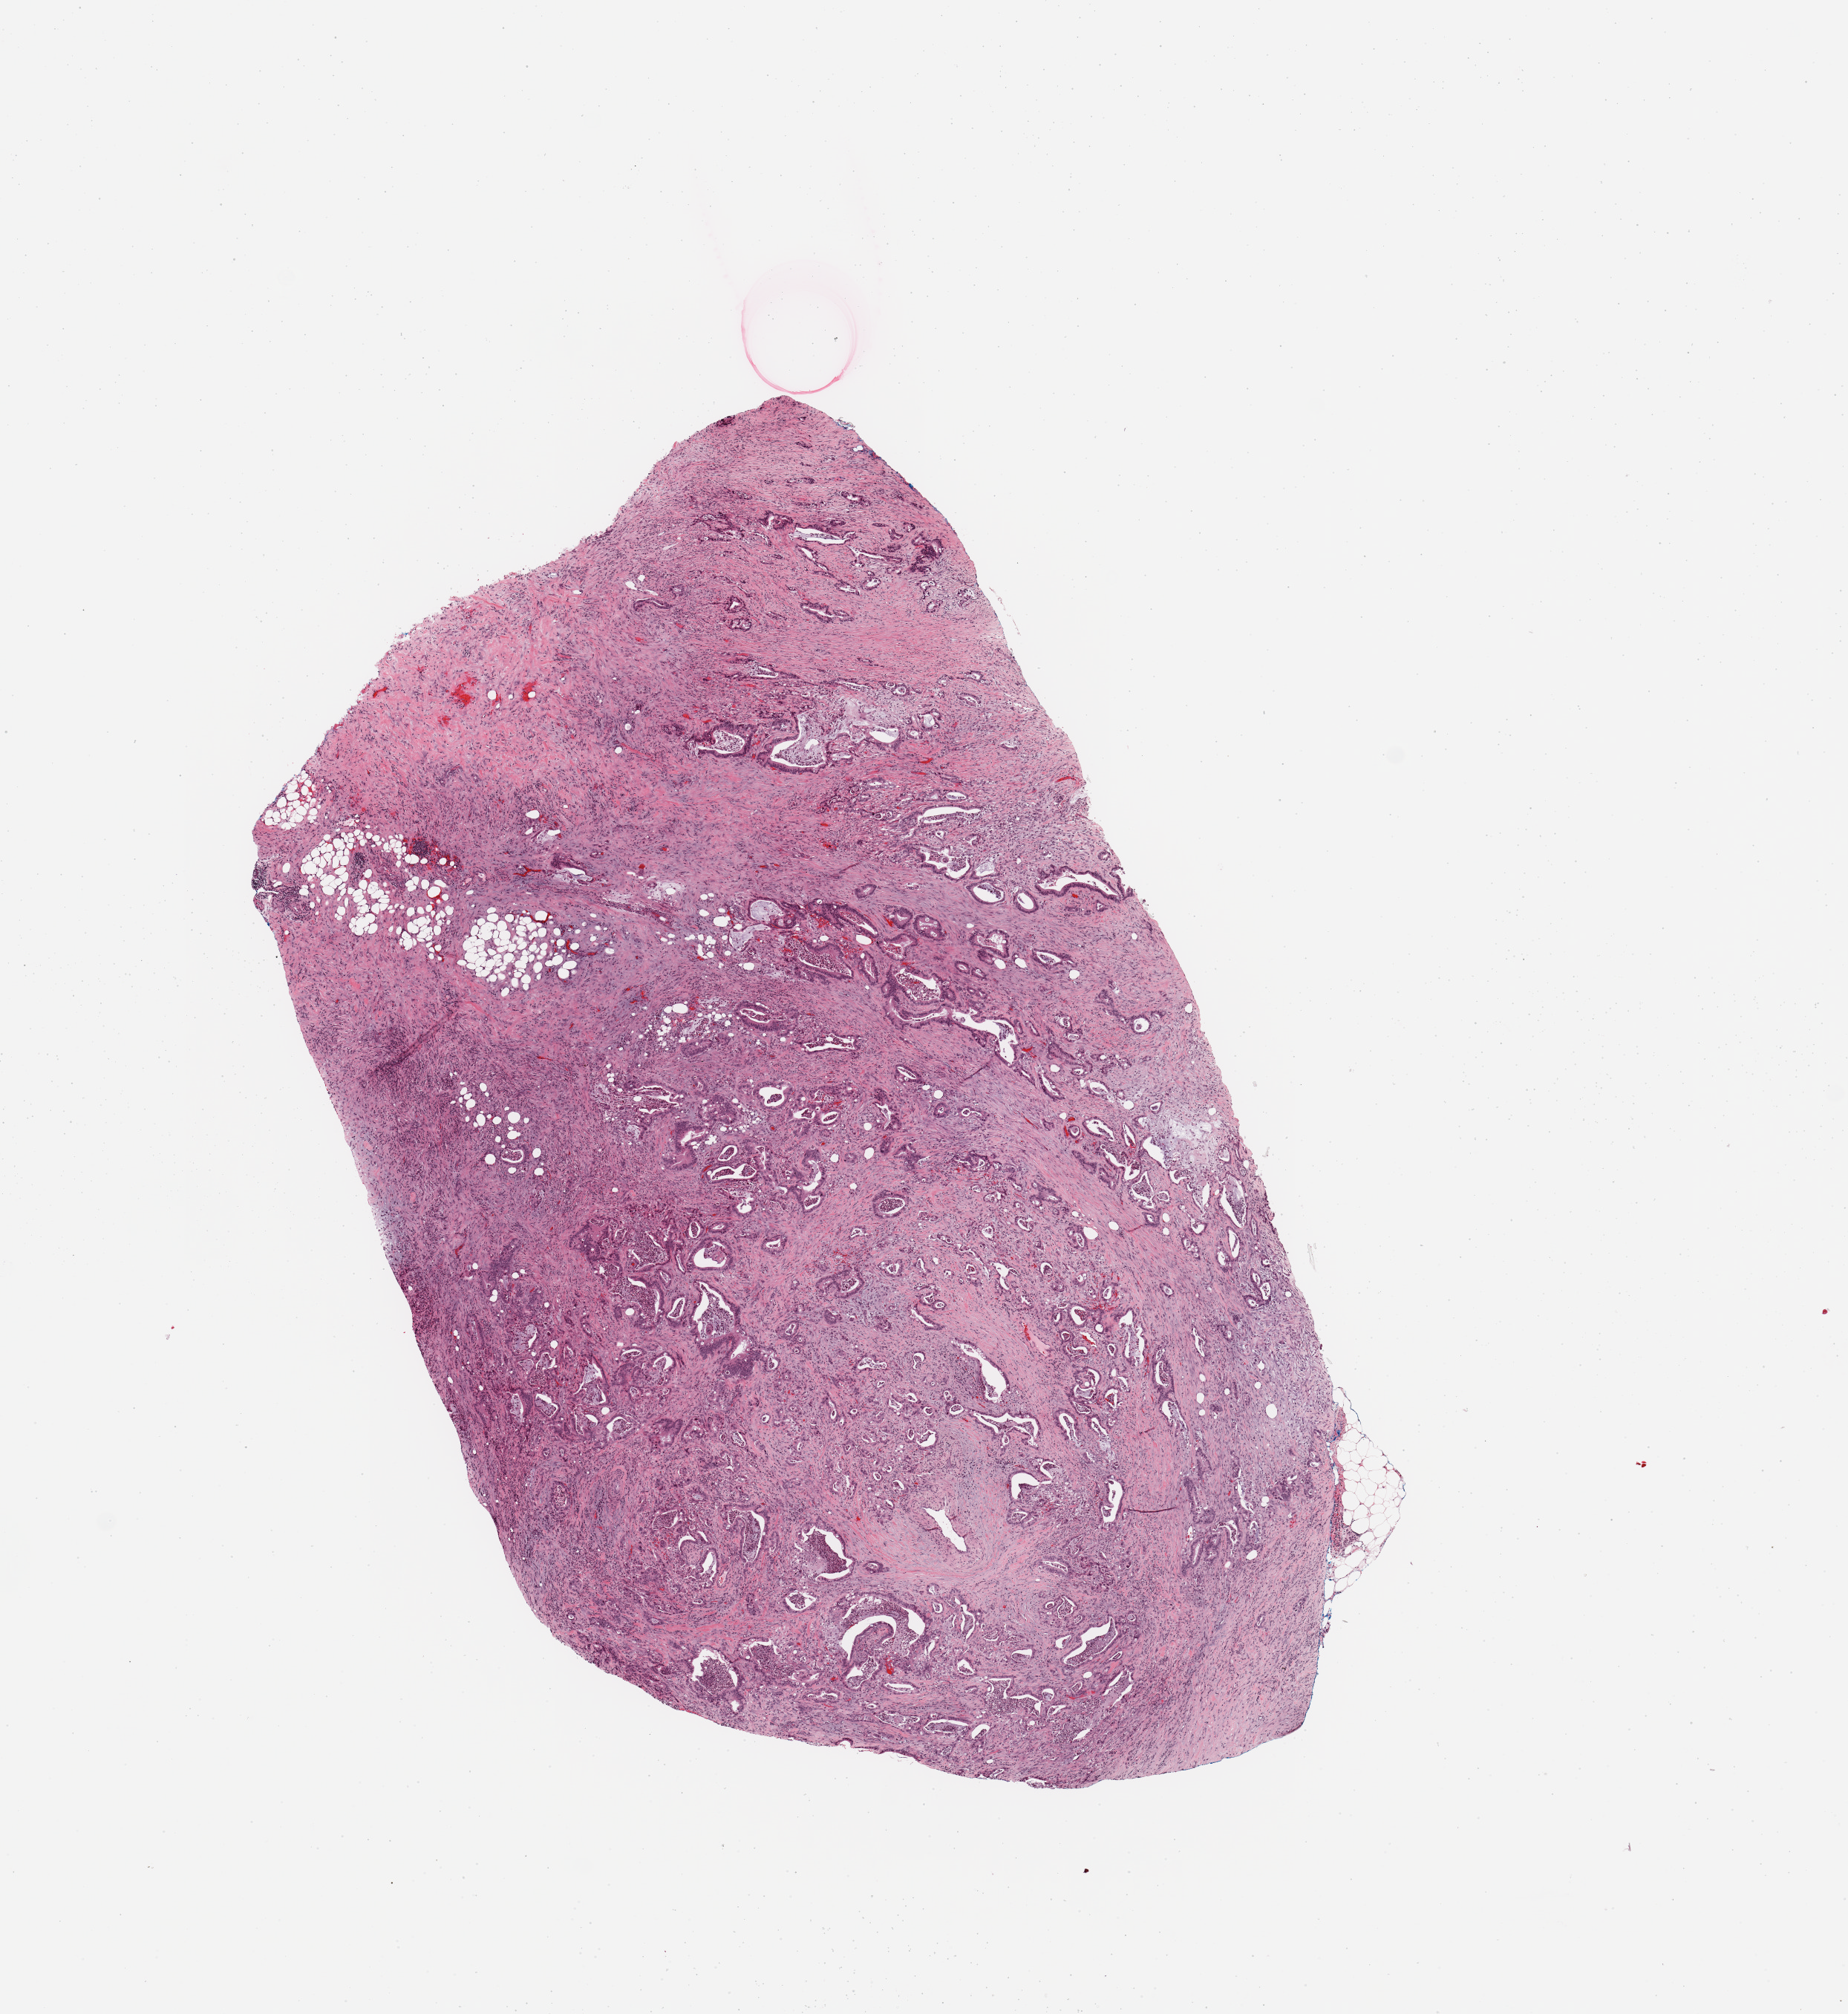
Digitized H&E tissue section (whole slide), a low-resolution overview of the entire scanned area, about 9.8 x 10.7 mm (slide scanned at 20x). Tumour tissue sample, pancreas. 58-year-old female patient.
Diagnosis: Infiltrating duct carcinoma, NOS.